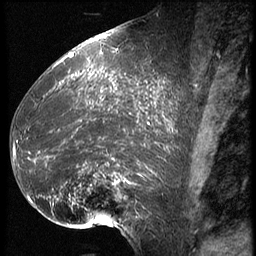
Breast MRI (dynamic contrast-enhanced), one sagittal slice. Slice 28 of 62 in the series (ordered by position). 3 images stored at this slice position (order not interpretable as contrast timing). 1.5 T. TE 4.2 ms, TR 9 ms. 2.5 mm slice thickness. 256 × 256 image matrix. Patient: female, 39 years. Case-level facts recorded for this patient, not image findings: setting: breast cancer imaged before/during neoadjuvant chemotherapy; receptor status: HER2-positive.
Structures marked on this image (semi-automatically segmented with operator editing):
- analysis volume of interest (the breast-tissue region the enhancement analysis was run in; not a lesion): bounding box [x1, y1, x2, y2] px = [16, 64, 171, 228]
- tumour enhancement mask (voxels above the 140 % enhancement threshold inside the analysis volume of interest): [16, 72, 171, 204]